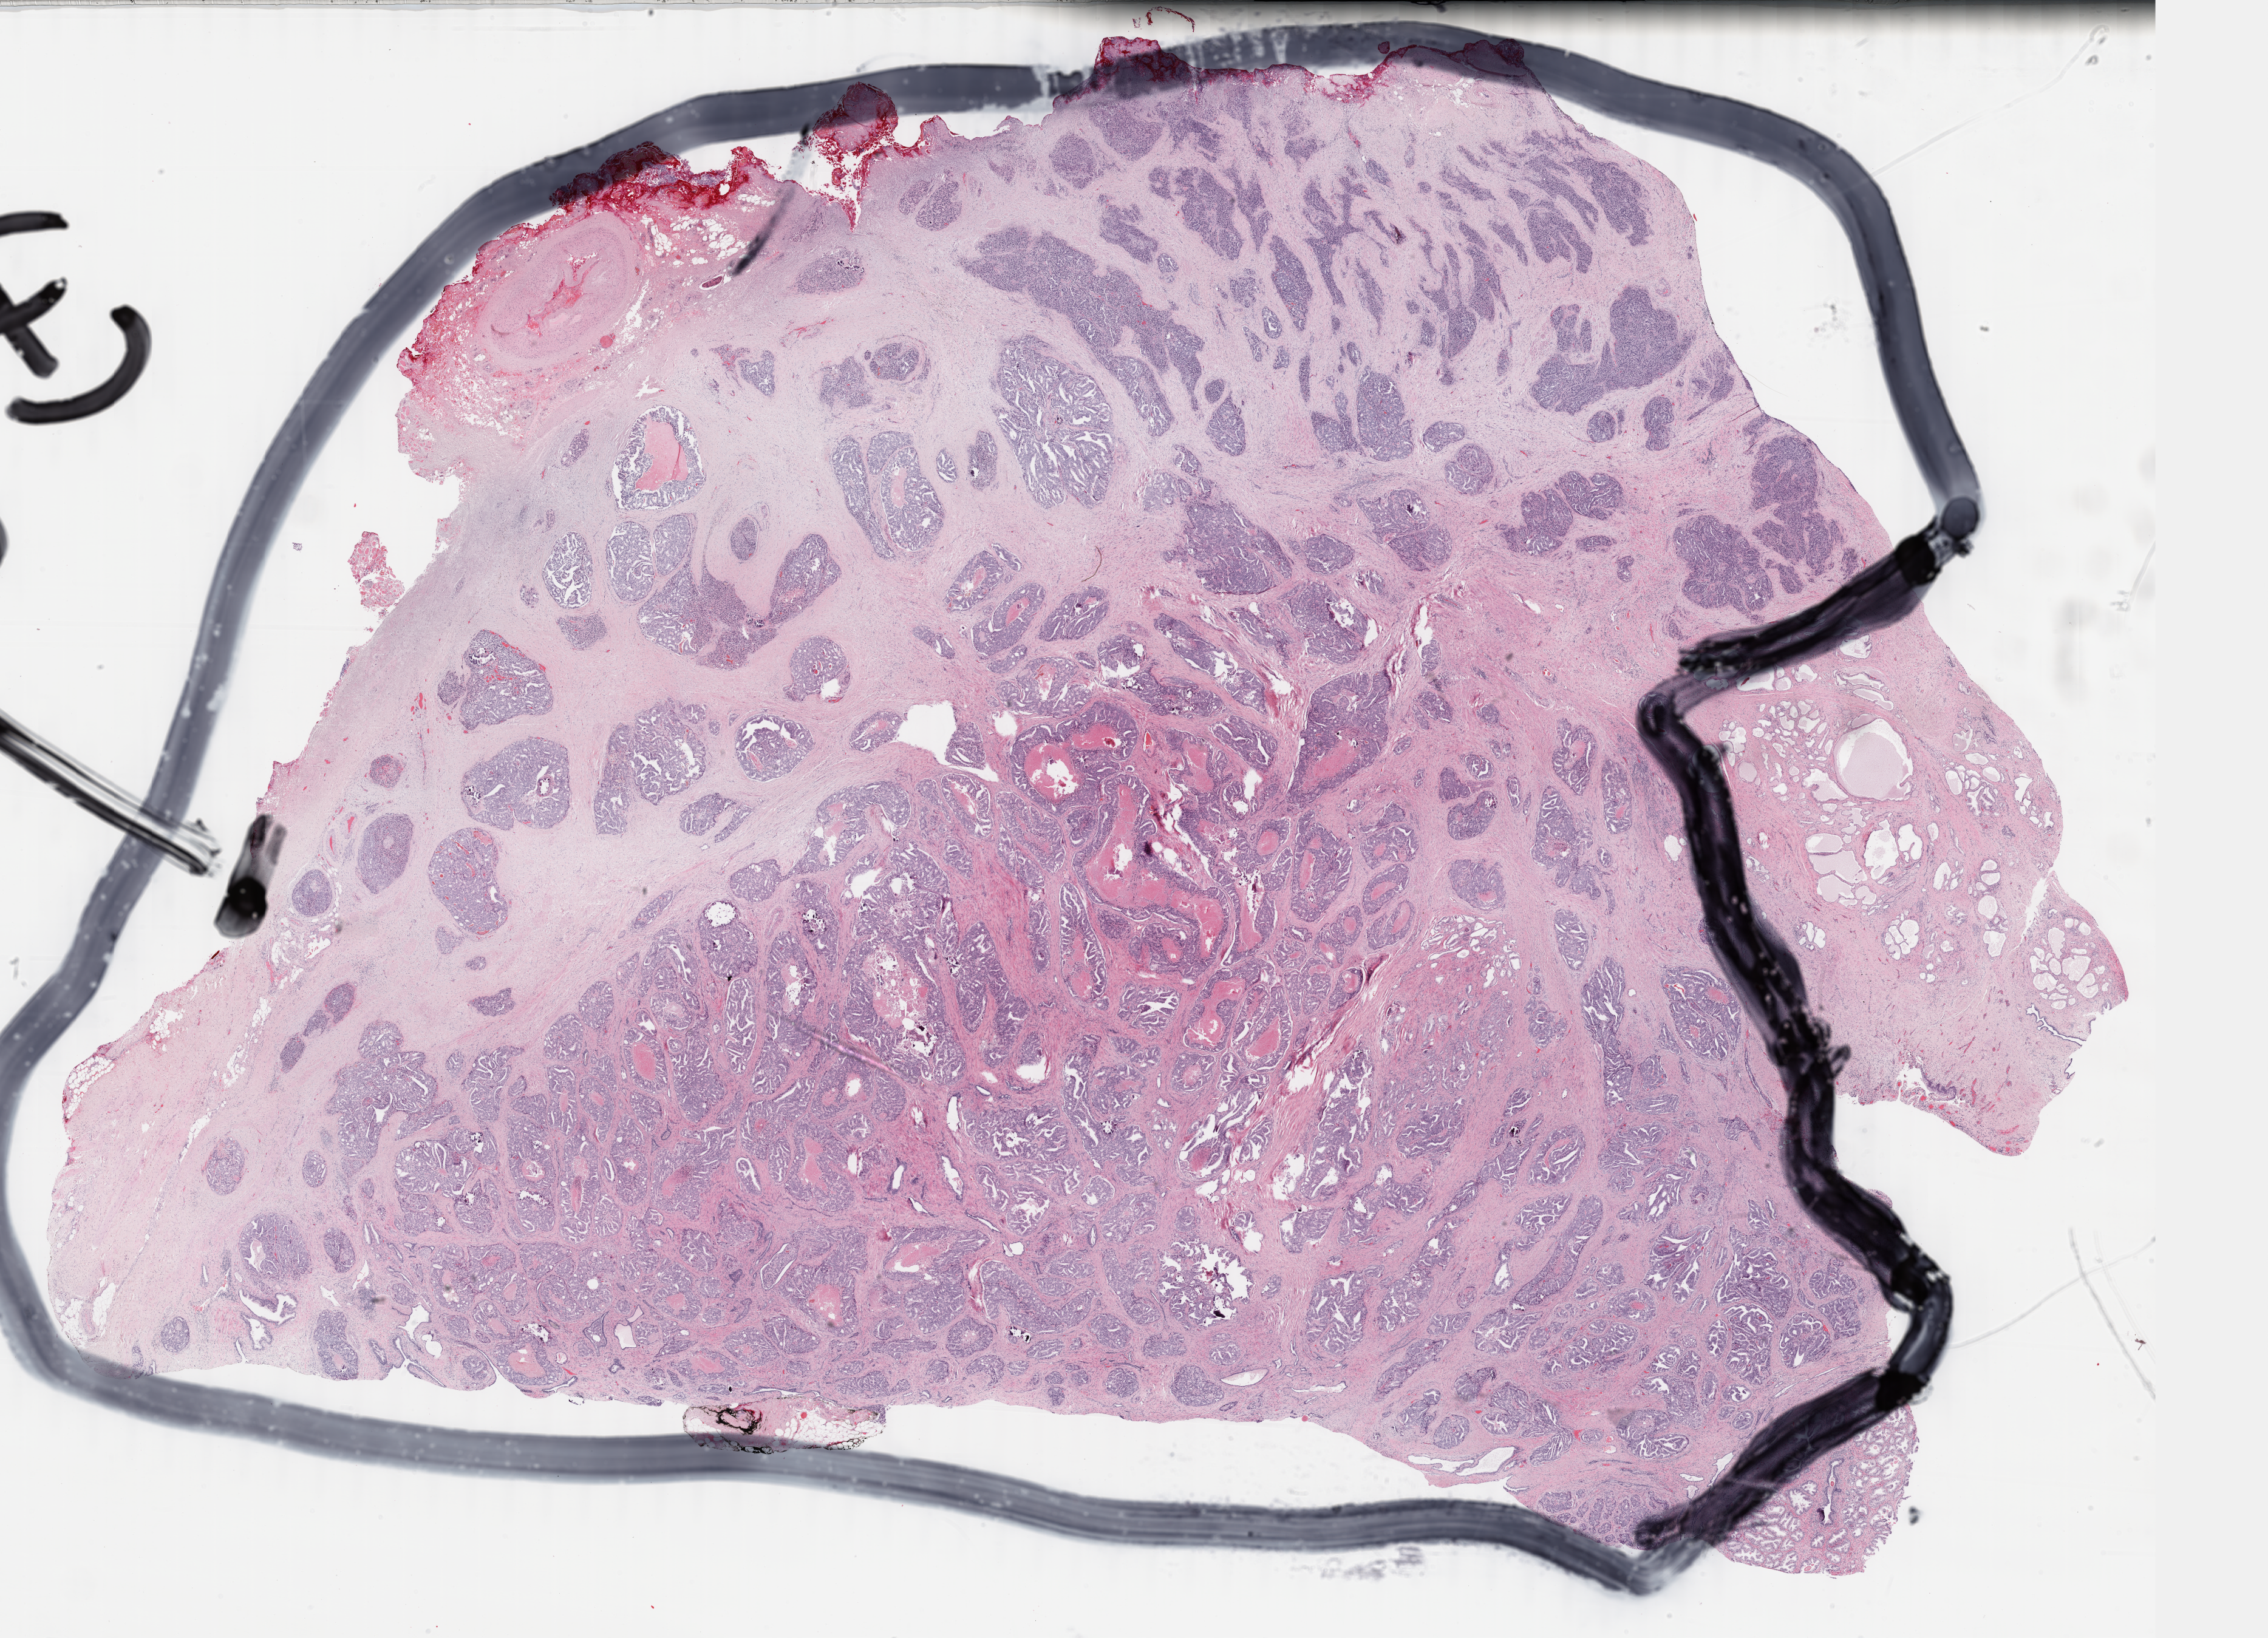
Hematoxylin and eosin (H&E) stained whole-slide image, low-resolution overview of the scanned area, about 29.7 x 21.5 mm; formalin-fixed paraffin-embedded (FFPE) diagnostic section; primary tumour sample from the prostate. Male, age 64 years at initial diagnosis. Gleason score: 9 (4+5).
* histologic diagnosis: Adenocarcinoma, NOS (prostate gland)
* laterality: bilateral